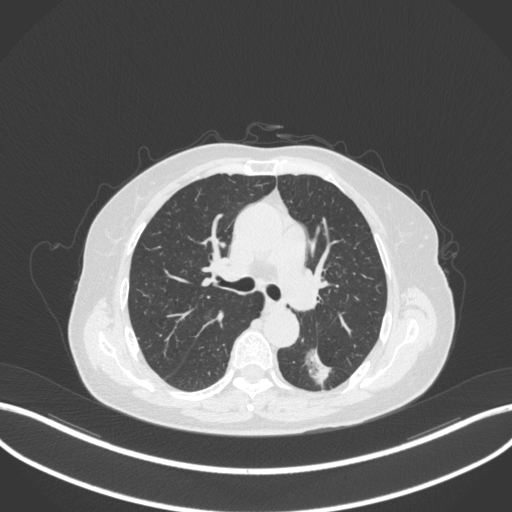
Chest CT, one axial slice; position 189 of 352 along the scan axis; reconstruction kernel B31f; lung window (W 1500 / L -600 HU); 512 × 512 image matrix, field of view 400 × 400 mm. Female patient, age 70 years. From the clinical record (not read from this slice): clinical TNM (as recorded): T1c N0 M0.
Annotated regions visible in this slice (rectangle marked by the reading radiologist):
- lung tumour (recorded histology: adenocarcinoma): box from (x=301, y=341) to (x=337, y=393) px